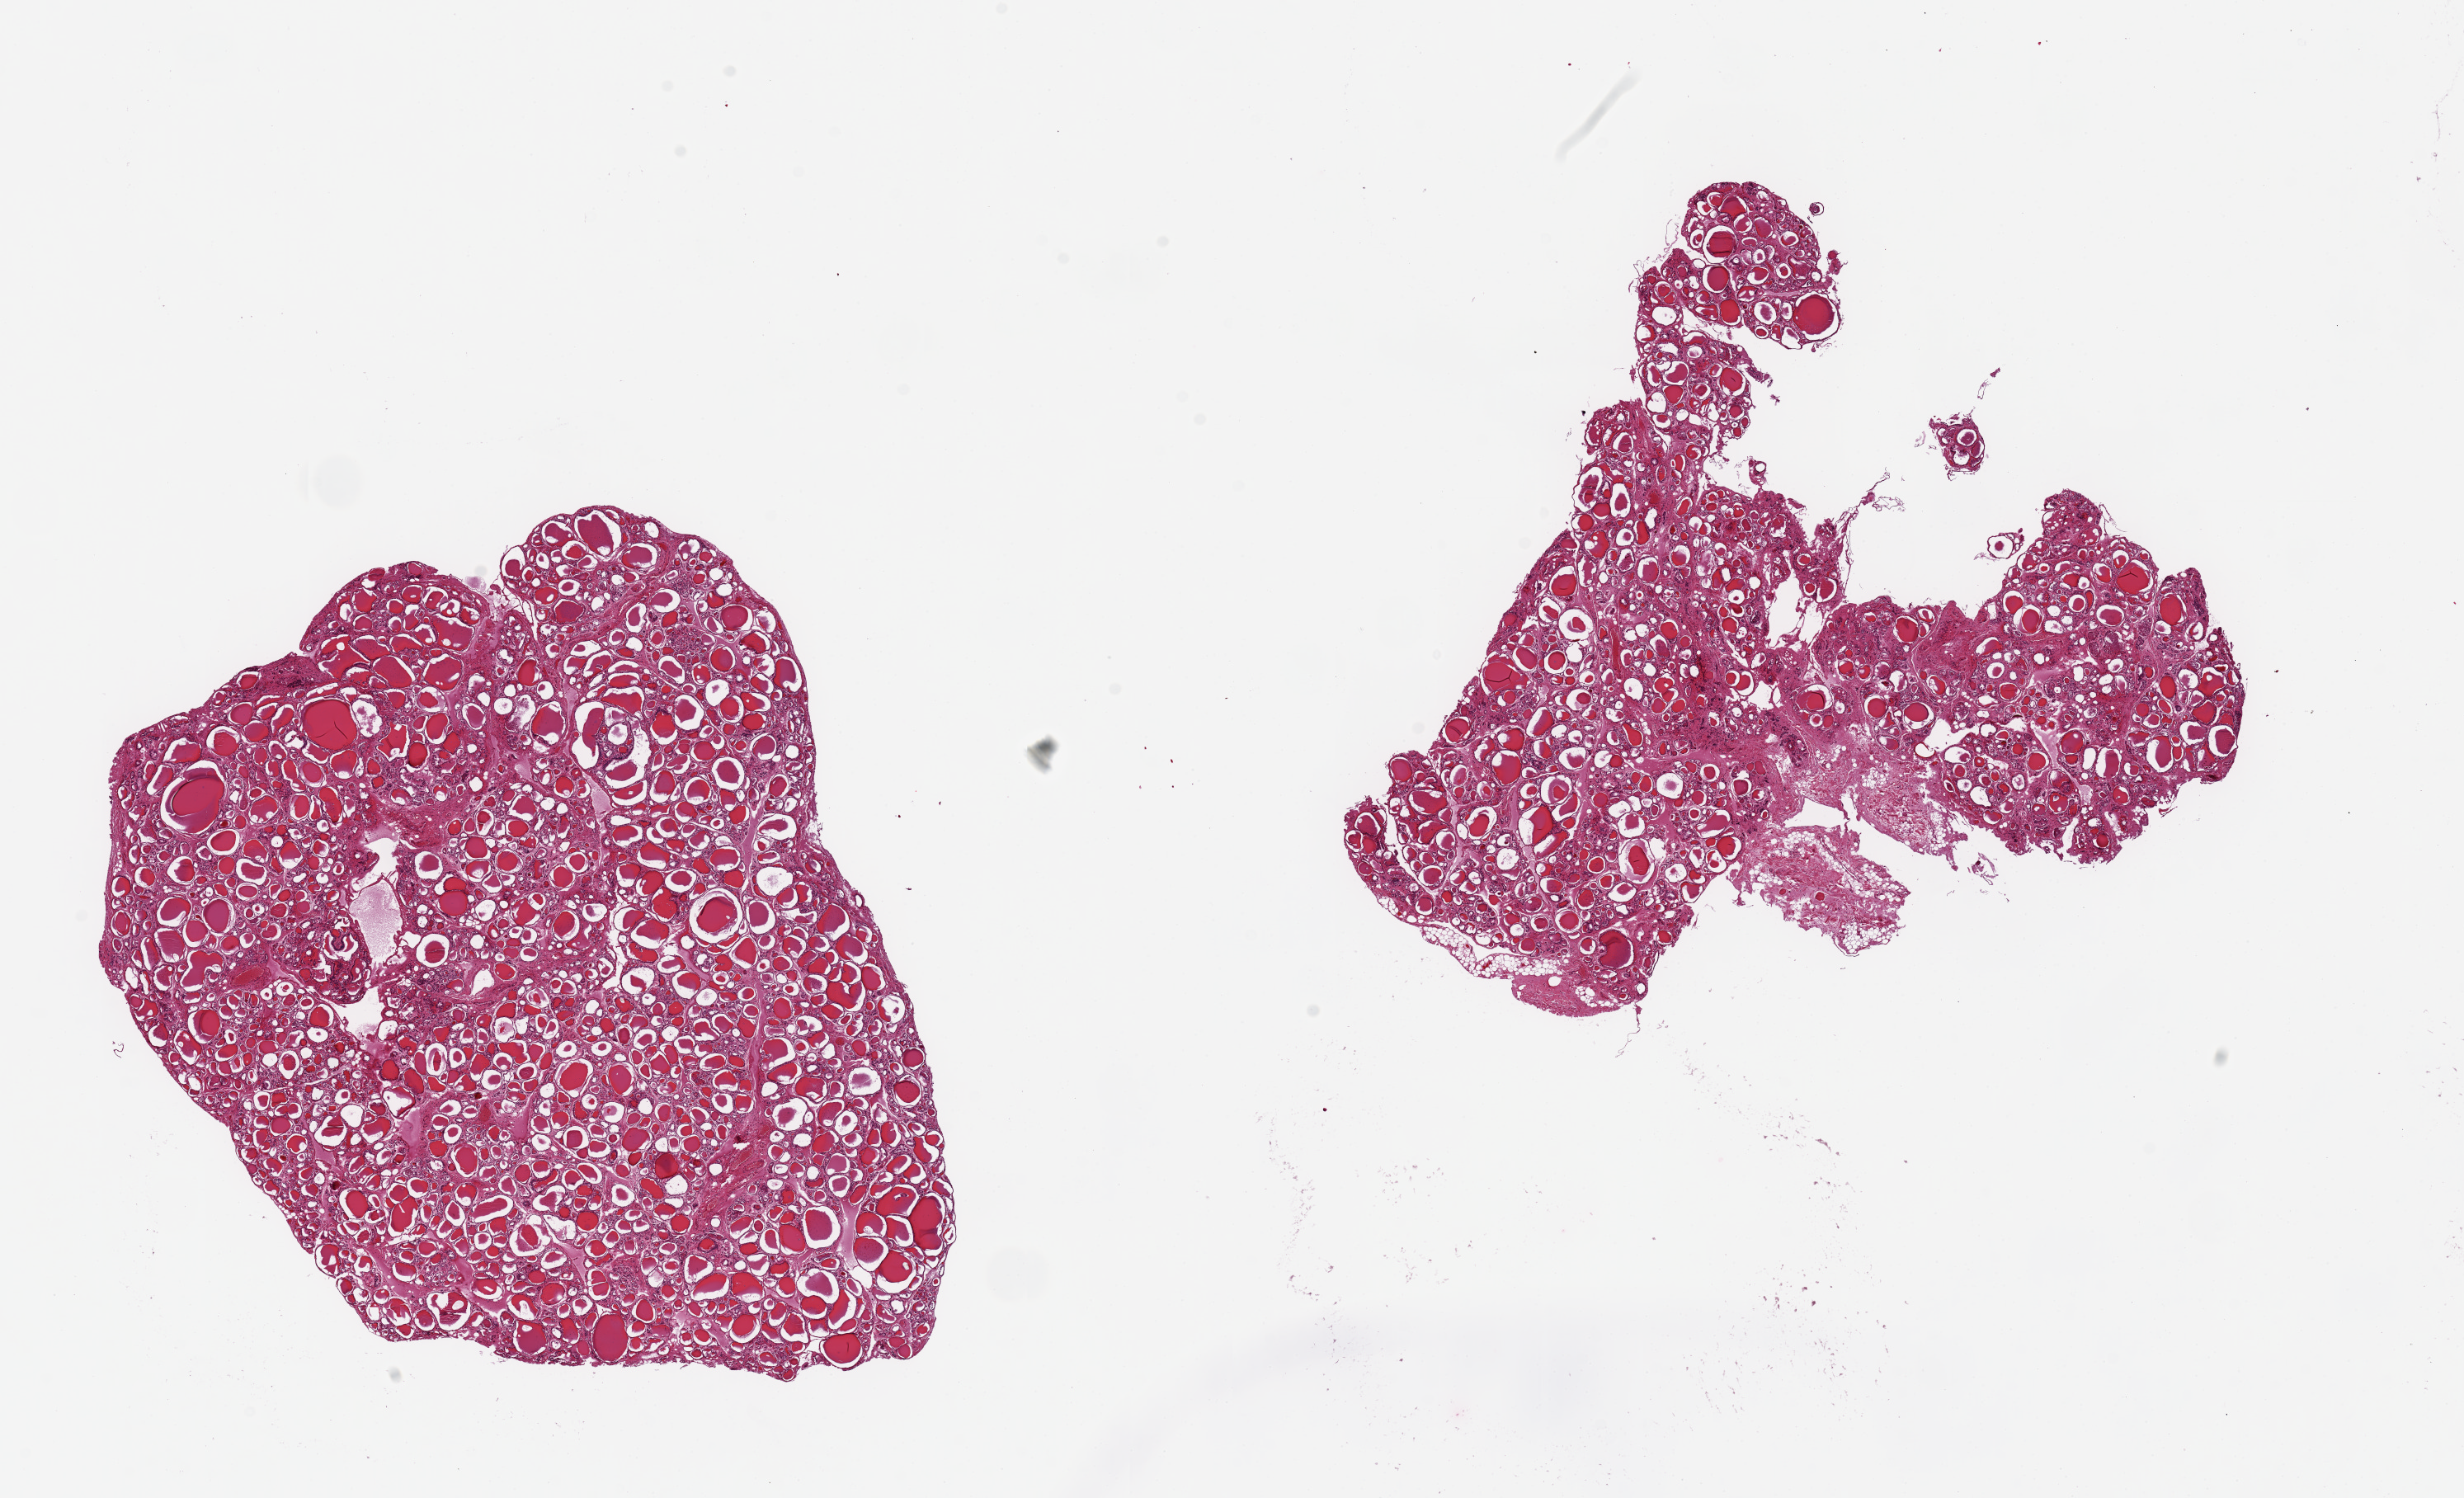
Whole-slide image, hematoxylin and eosin (H&E) stain, a low-resolution overview of the entire scanned area, about 23.6 x 14.4 mm, PAXgene-fixed, paraffin-embedded tissue, sampled site (target tissue): thyroid, tissue donor sample.
Reviewer comment on this tissue sample: 2 pieces, 9x7 & 8x7mm; 10% stroma at edge of smaller piece.